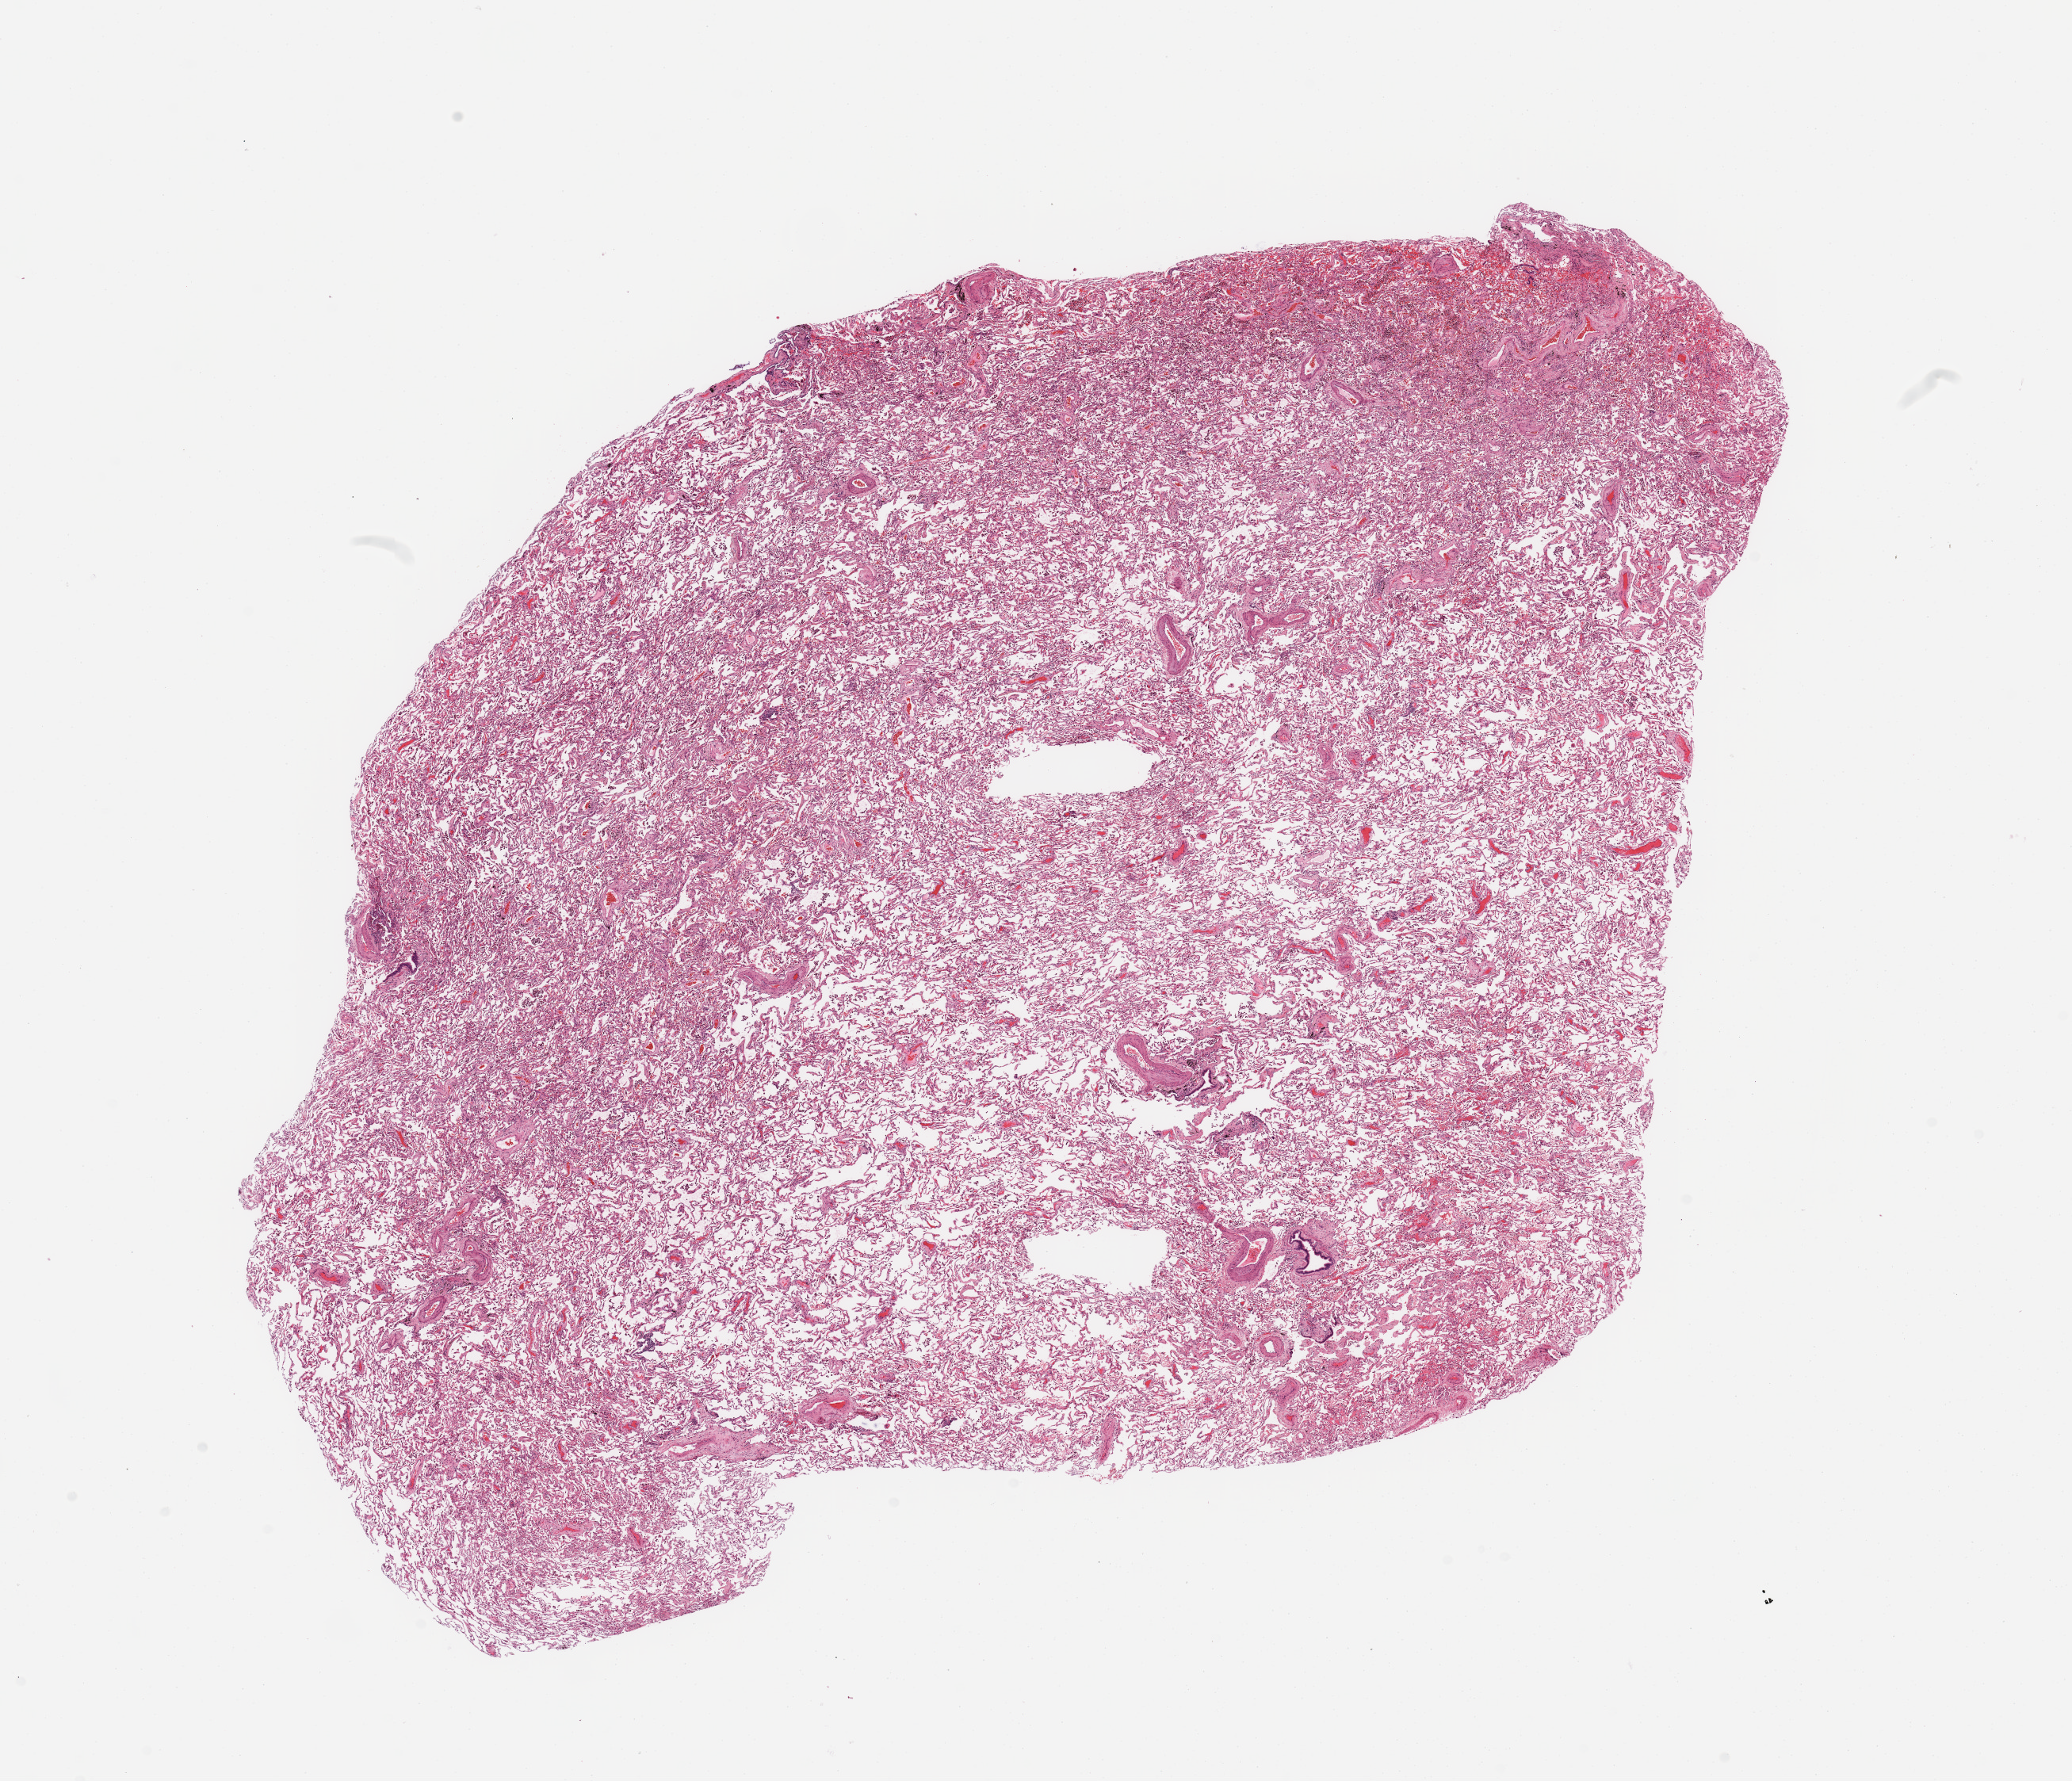
Whole-slide histology image, H&E-stained — low-resolution overview of the scanned area, about 20.7 x 17.8 mm (slide scanned at 20x), normal (non-tumour) tissue sample, sampled site: lung. Male, 64 y/o.
• this section: normal (non-tumour) tissue from the same patient
• patient diagnosis: Adenocarcinoma, NOS